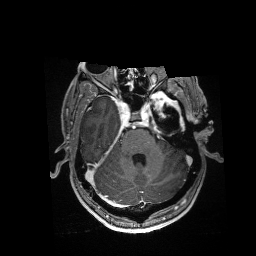
Brain MRI from a brain-tumour surgery series, one axial slice. Position 115 of 176 along the scan axis. T1-weighted post-contrast. 256 × 256 image matrix. Case-level facts recorded for this patient, not image findings: histopathology: Glioblastoma; WHO grade: 4; IDH mutation: no; tumour location: Left Anterior/Superior Temporal.
Annotated regions visible in this slice (outlined manually by an expert reader):
- residual tumour: box from (x=152, y=91) to (x=180, y=113) px